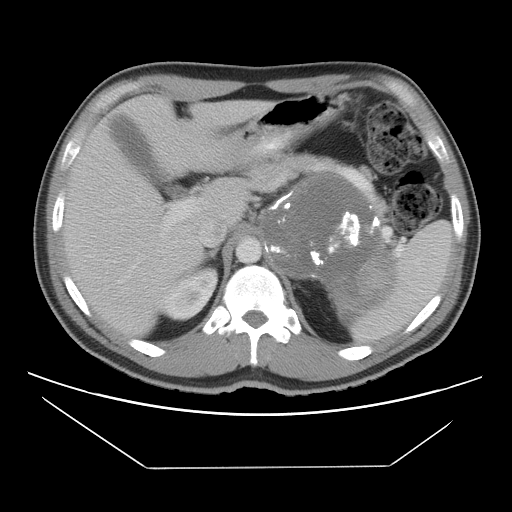
Contrast-enhanced abdominal CT, one axial slice; slice 74 of 131 in the series (ordered by position); soft-tissue window (W 400 / L 40 HU); 5 mm slice thickness; 512 × 512 image matrix, field of view 396 × 396 mm. Male patient, age 44 years. From the clinical record (not read from this slice): diagnosis: adrenocortical carcinoma; tumour side: left adrenal; tumour size at pathology: 15.5 cm; Ki-67 index: 6 %; stage (as recorded): 2.
Annotated regions visible in this slice (semi-automatically segmented with operator editing):
- mass: bounding box <262,176,392,325> (left, top, right, bottom; pixels)